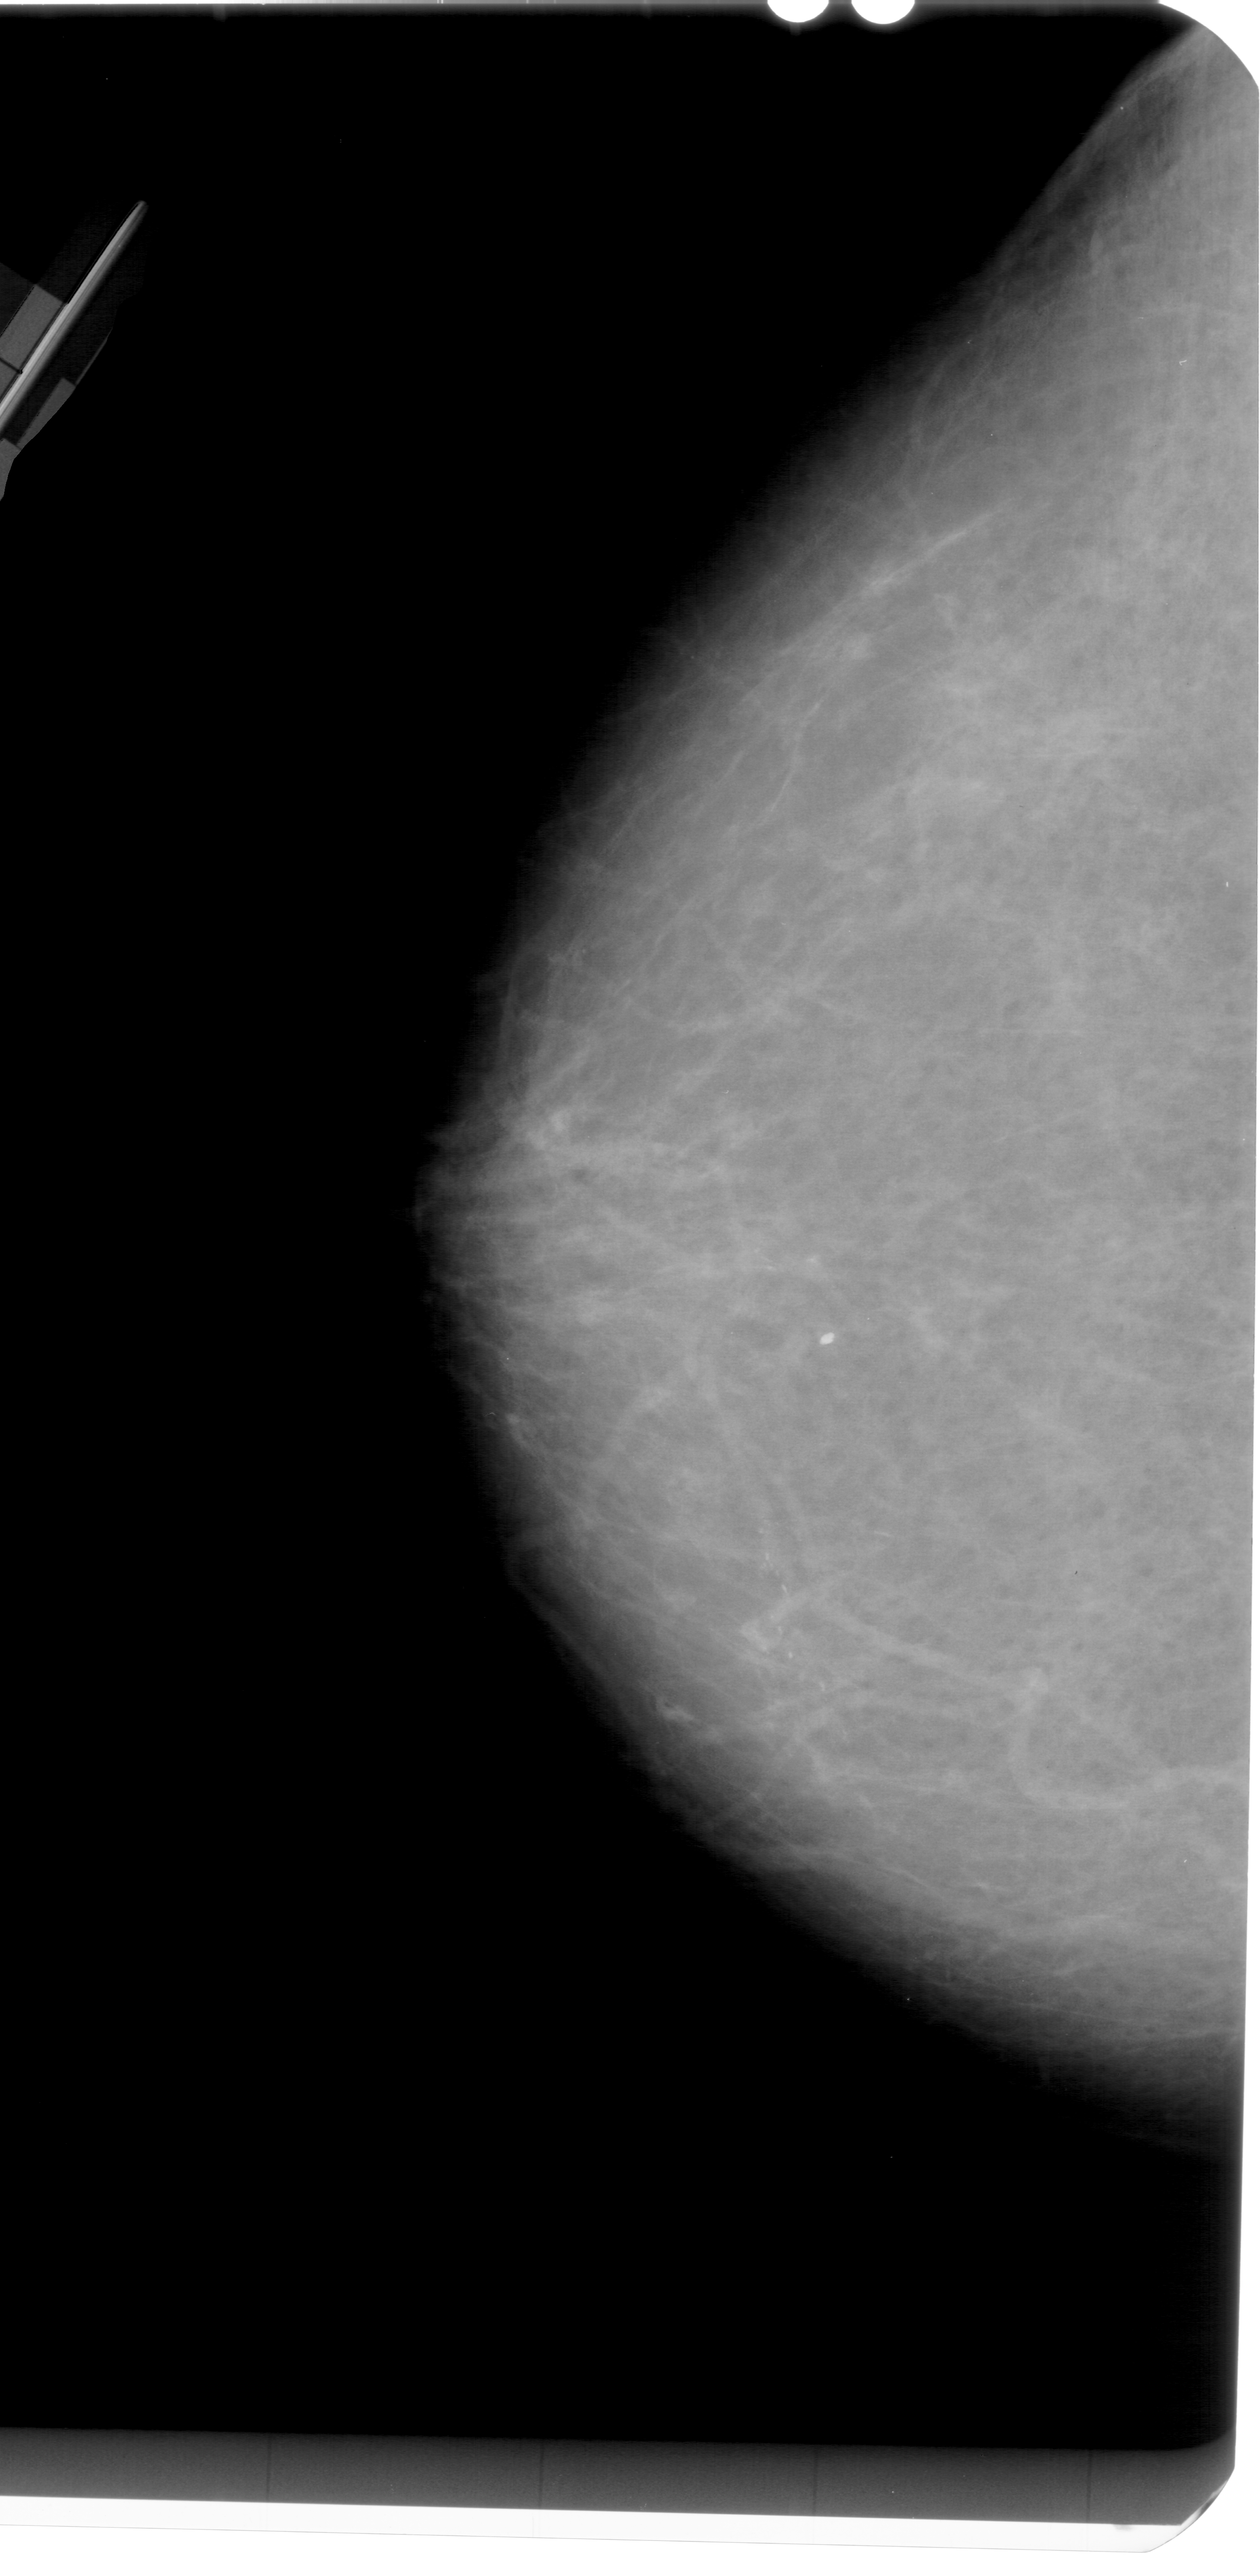
Digitized screen-film mammogram; left breast; CC view; 1260 × 2576 image matrix.
Expert-marked regions of interest on this film, with their recorded descriptors:
- calcifications, morphology pleomorphic, distribution linear; BI-RADS assessment category 4; pathology (as recorded): malignant: bounding box <666,1413,892,1804> (left, top, right, bottom; pixels)